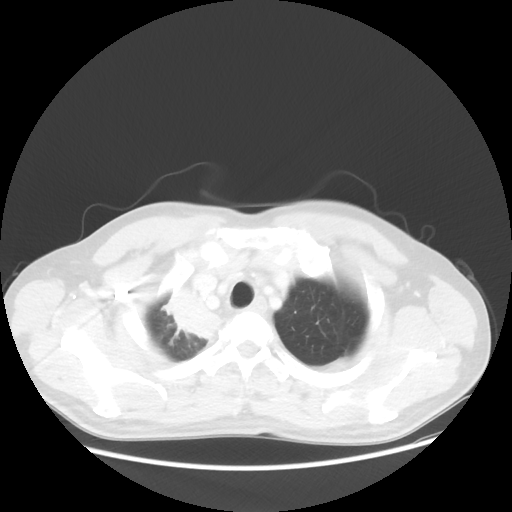
Chest CT, one axial slice; position 48 of 56 along the scan axis; 100 kVp; lung window (W 1500 / L -600 HU); 5 mm slice thickness; 512 × 512 image matrix, field of view 398 × 398 mm. Male patient, age 60 years. From the clinical record (not read from this slice): clinical TNM (as recorded): T2a N1 M0.
Annotated regions visible in this slice (rectangle marked by the reading radiologist):
- lung tumour (recorded histology: squamous cell carcinoma): bounding box [x1, y1, x2, y2] px = [151, 271, 233, 354]